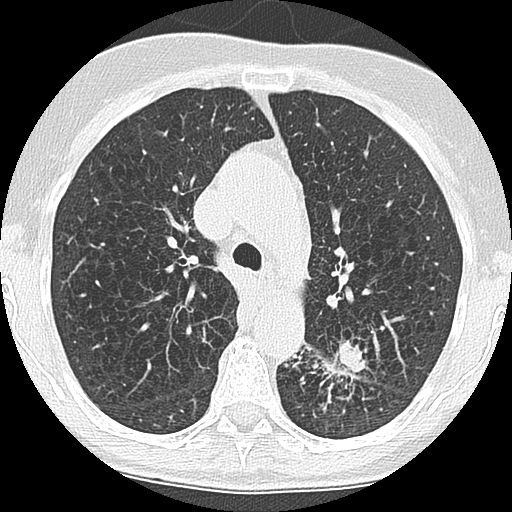
Low-dose screening chest CT, one axial slice; position 121 of 171 along the scan axis; lung window (W 1500 / L -600 HU); 2.5 mm slice thickness; 512 × 512 image matrix, field of view 280 × 280 mm.
Annotated regions visible in this slice (manually delineated by an expert):
- lesion 1 (tumor, lower lobe of left lung): bounding box [x1, y1, x2, y2] px = [331, 340, 368, 372]